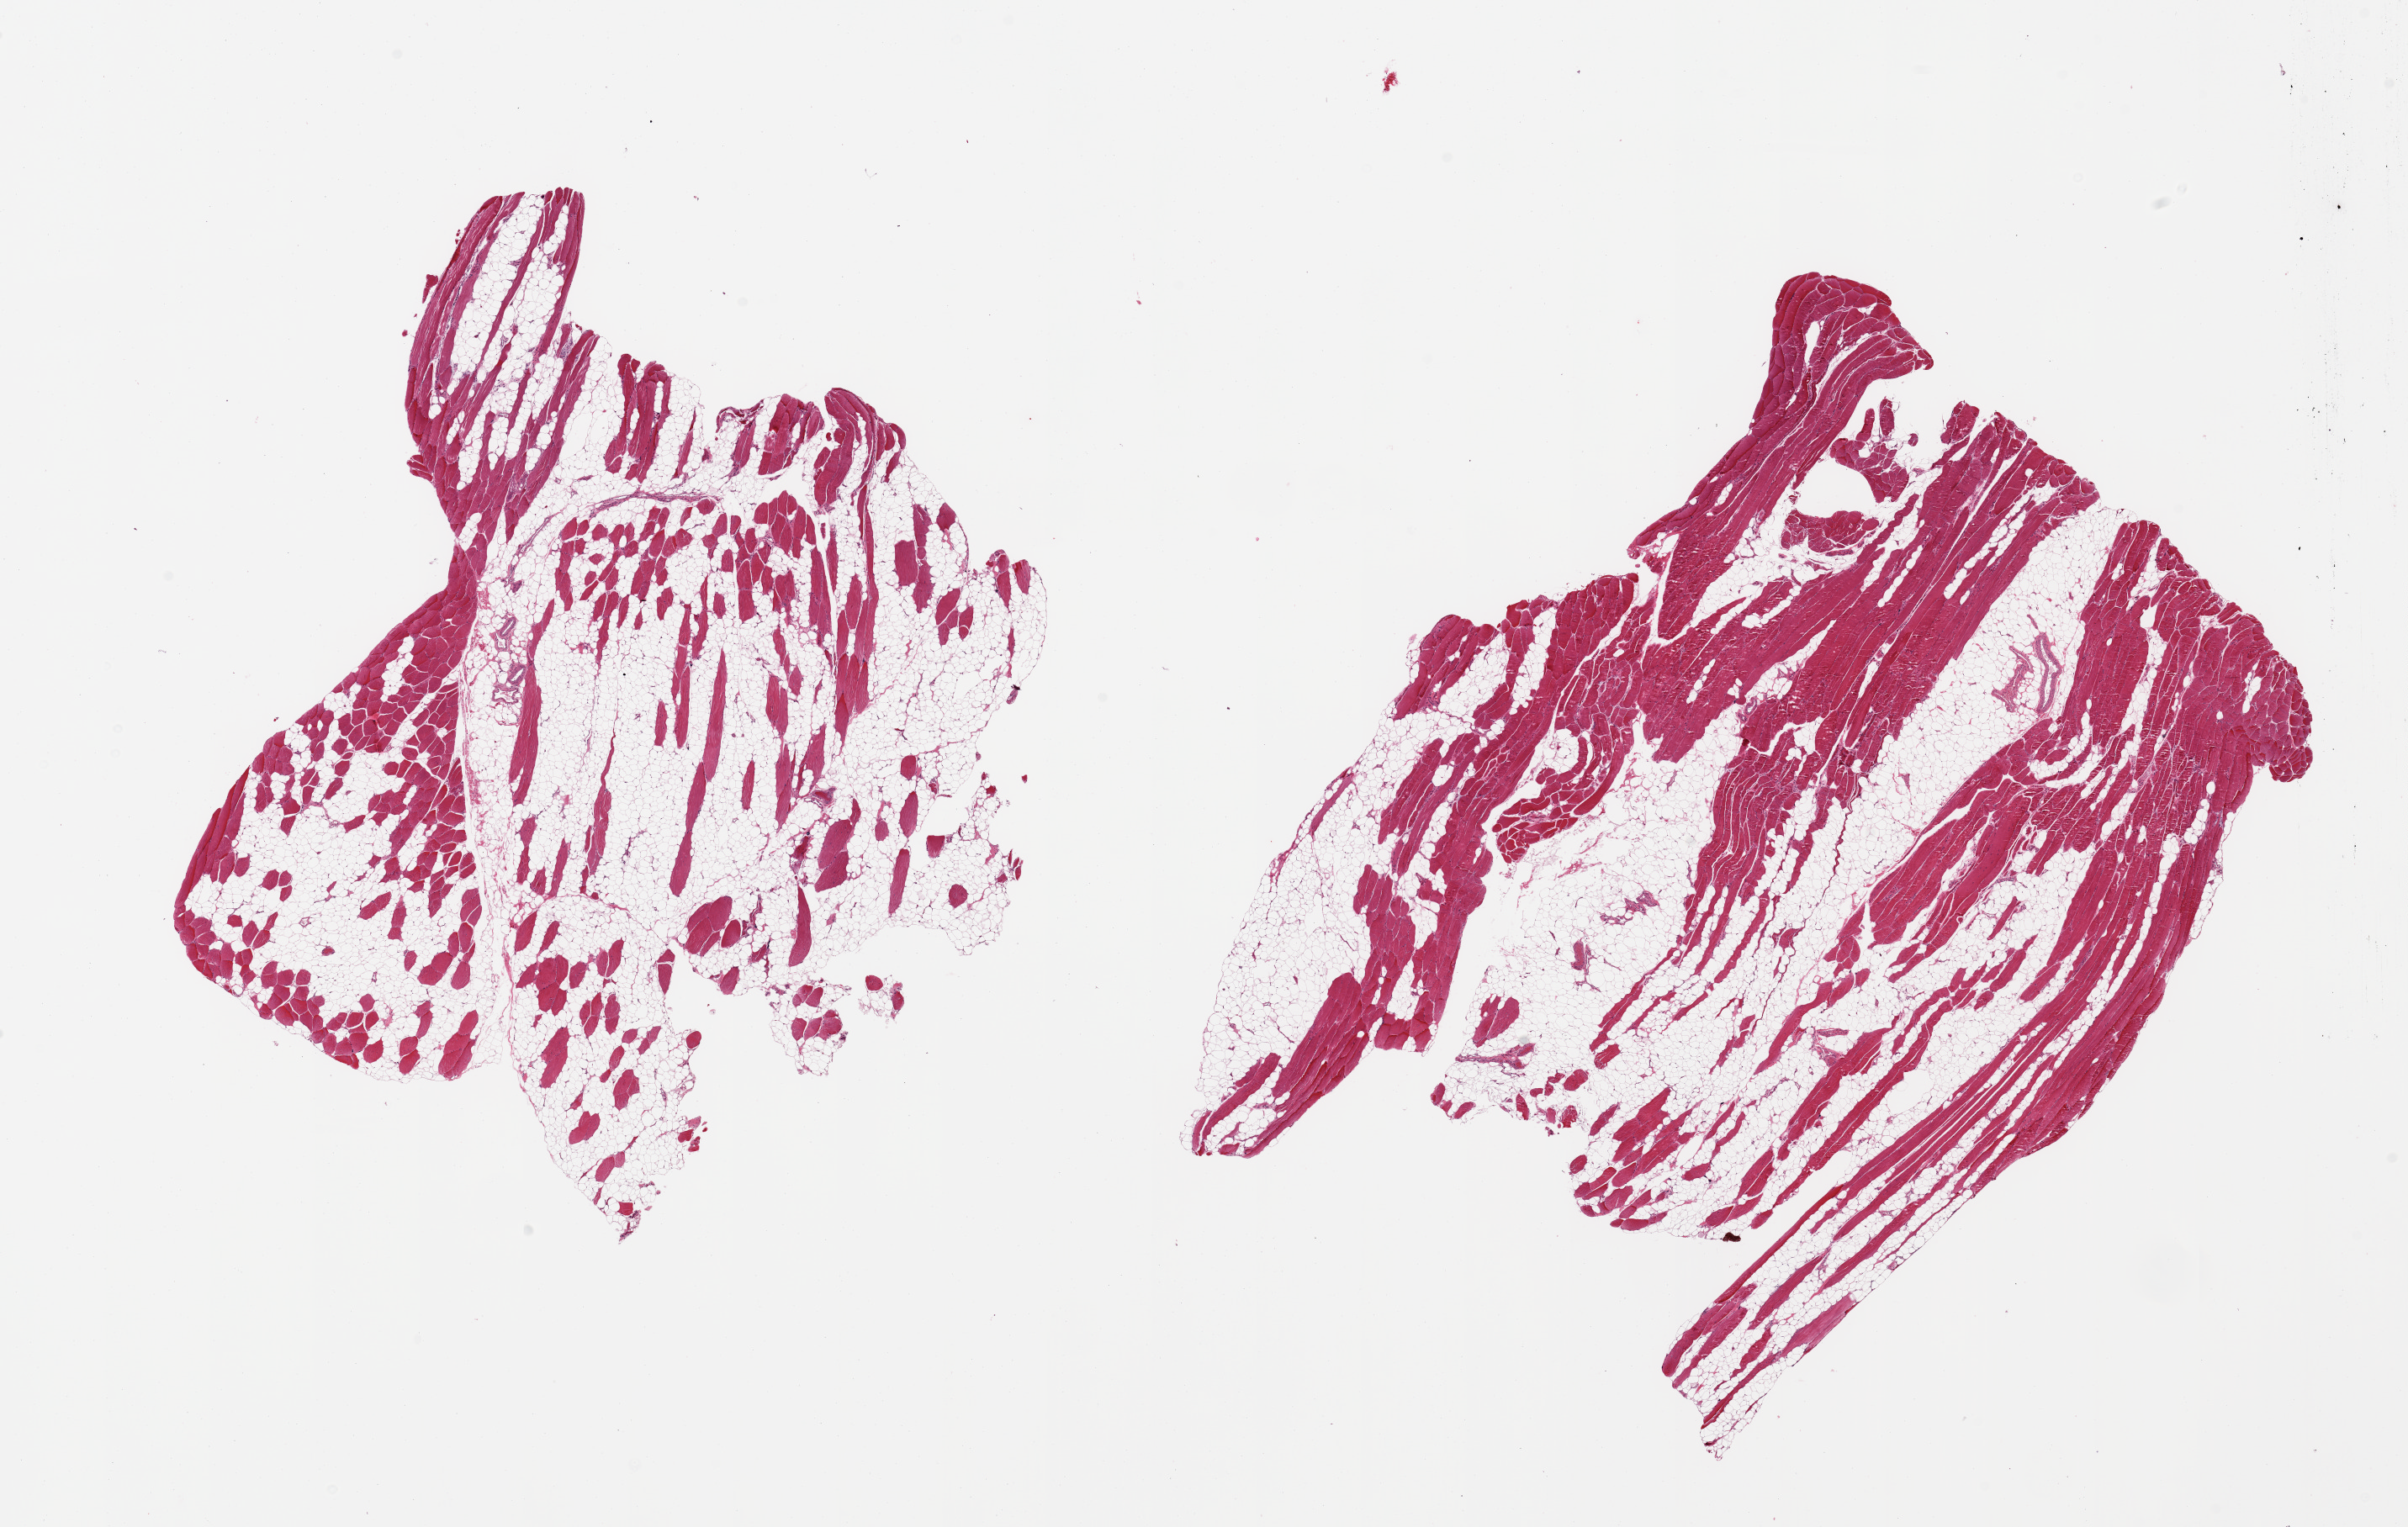
Hematoxylin and eosin (H&E) whole-slide image — shown as a low-resolution overview of the whole scanned area (about 22.6 x 14.4 mm, from a 20x scan), PAXgene-fixed paraffin-embedded (PFPE) section, sampled site (target tissue): skeletal muscle, donor tissue sample. Donor sex: female.
* reviewer comment on this tissue sample: 2 pieces; extensive replacement of muscular tissue by fat, 50-80%